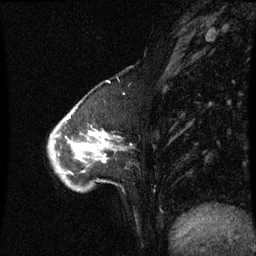
Breast MRI (dynamic contrast-enhanced), one sagittal slice. Slice 20 of 60 in the series (ordered by position). Dynamic contrast-enhanced series, image 2 of 3 at this slice position (ordered by acquisition). 1.5 T. TE 4.2 ms, TR 8.9 ms. 2 mm slice thickness. 256 × 256 image matrix, field of view 200 × 200 mm. Patient: female, 50 years. Case-level facts recorded for this patient, not image findings: setting: breast cancer imaged before/during neoadjuvant chemotherapy; receptor status: HR-positive, HER2-negative.
Outlined on this slice (semi-automatically segmented with operator editing):
- analysis volume of interest (the breast-tissue region the enhancement analysis was run in; not a lesion): box from (x=50, y=102) to (x=117, y=191) px
- tumour enhancement mask (voxels above the 70 % enhancement threshold inside the analysis volume of interest): (x=90, y=132)–(x=106, y=163)